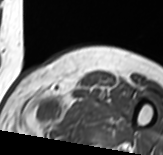
MRI of an extremity soft-tissue mass, one axial slice. Position 51 of 65 along the scan axis. MR volume resampled by the dataset authors to the PET/CT grid (not the native acquisition matrix). 3.27 mm slice thickness. 163 × 155 image matrix. Female patient. From the clinical record (not read from this slice): histological type: pleomorphic leiomyosarcoma; grade: high; site of the primary tumour: left thigh.
Annotated regions visible in this slice (expert contour drawn on MRI and transferred to this co-registered scan by the dataset authors):
- gross tumour volume including surrounding oedema: bounding box (x1, y1, x2, y2) in pixels: (32, 95, 88, 130)